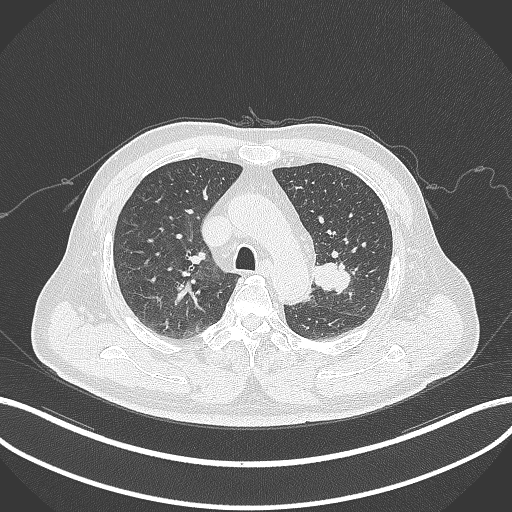
Chest CT, one axial slice. Slice 214 of 286 in the series (ordered by position). 120 kVp. Lung window (W 1500 / L -600 HU). 512 × 512 image matrix, field of view 400 × 400 mm. Patient: male, 67 years. Case-level facts recorded for this patient, not image findings: clinical TNM (as recorded): T2a N1 M0.
Outlined on this slice (rectangle marked by the reading radiologist):
- lung tumour (recorded histology: adenocarcinoma): box from (x=309, y=256) to (x=353, y=295) px